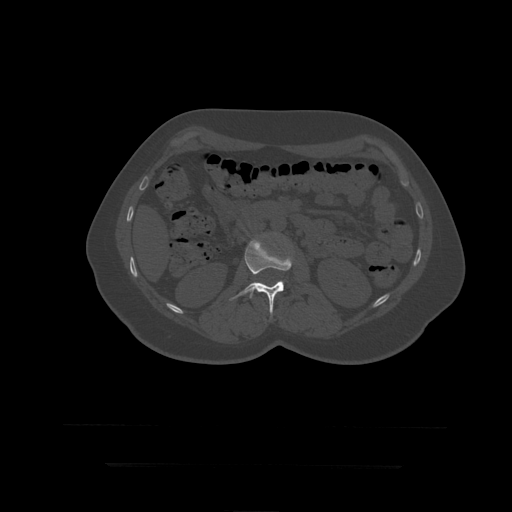
CT including the spine, one axial slice. Position 145 of 399 along the scan axis. 120 kVp. Bone window (W 1800 / L 400 HU). 1.25 mm slice thickness. 512 × 512 image matrix, field of view 450 × 450 mm. Patient age 41 years. Case-level facts recorded for this patient, not image findings: primary cancer: breast.
Structures marked on this image (semi-automatically segmented with operator editing):
- L2 vertebra: bounding box <230,240,292,317> (left, top, right, bottom; pixels)